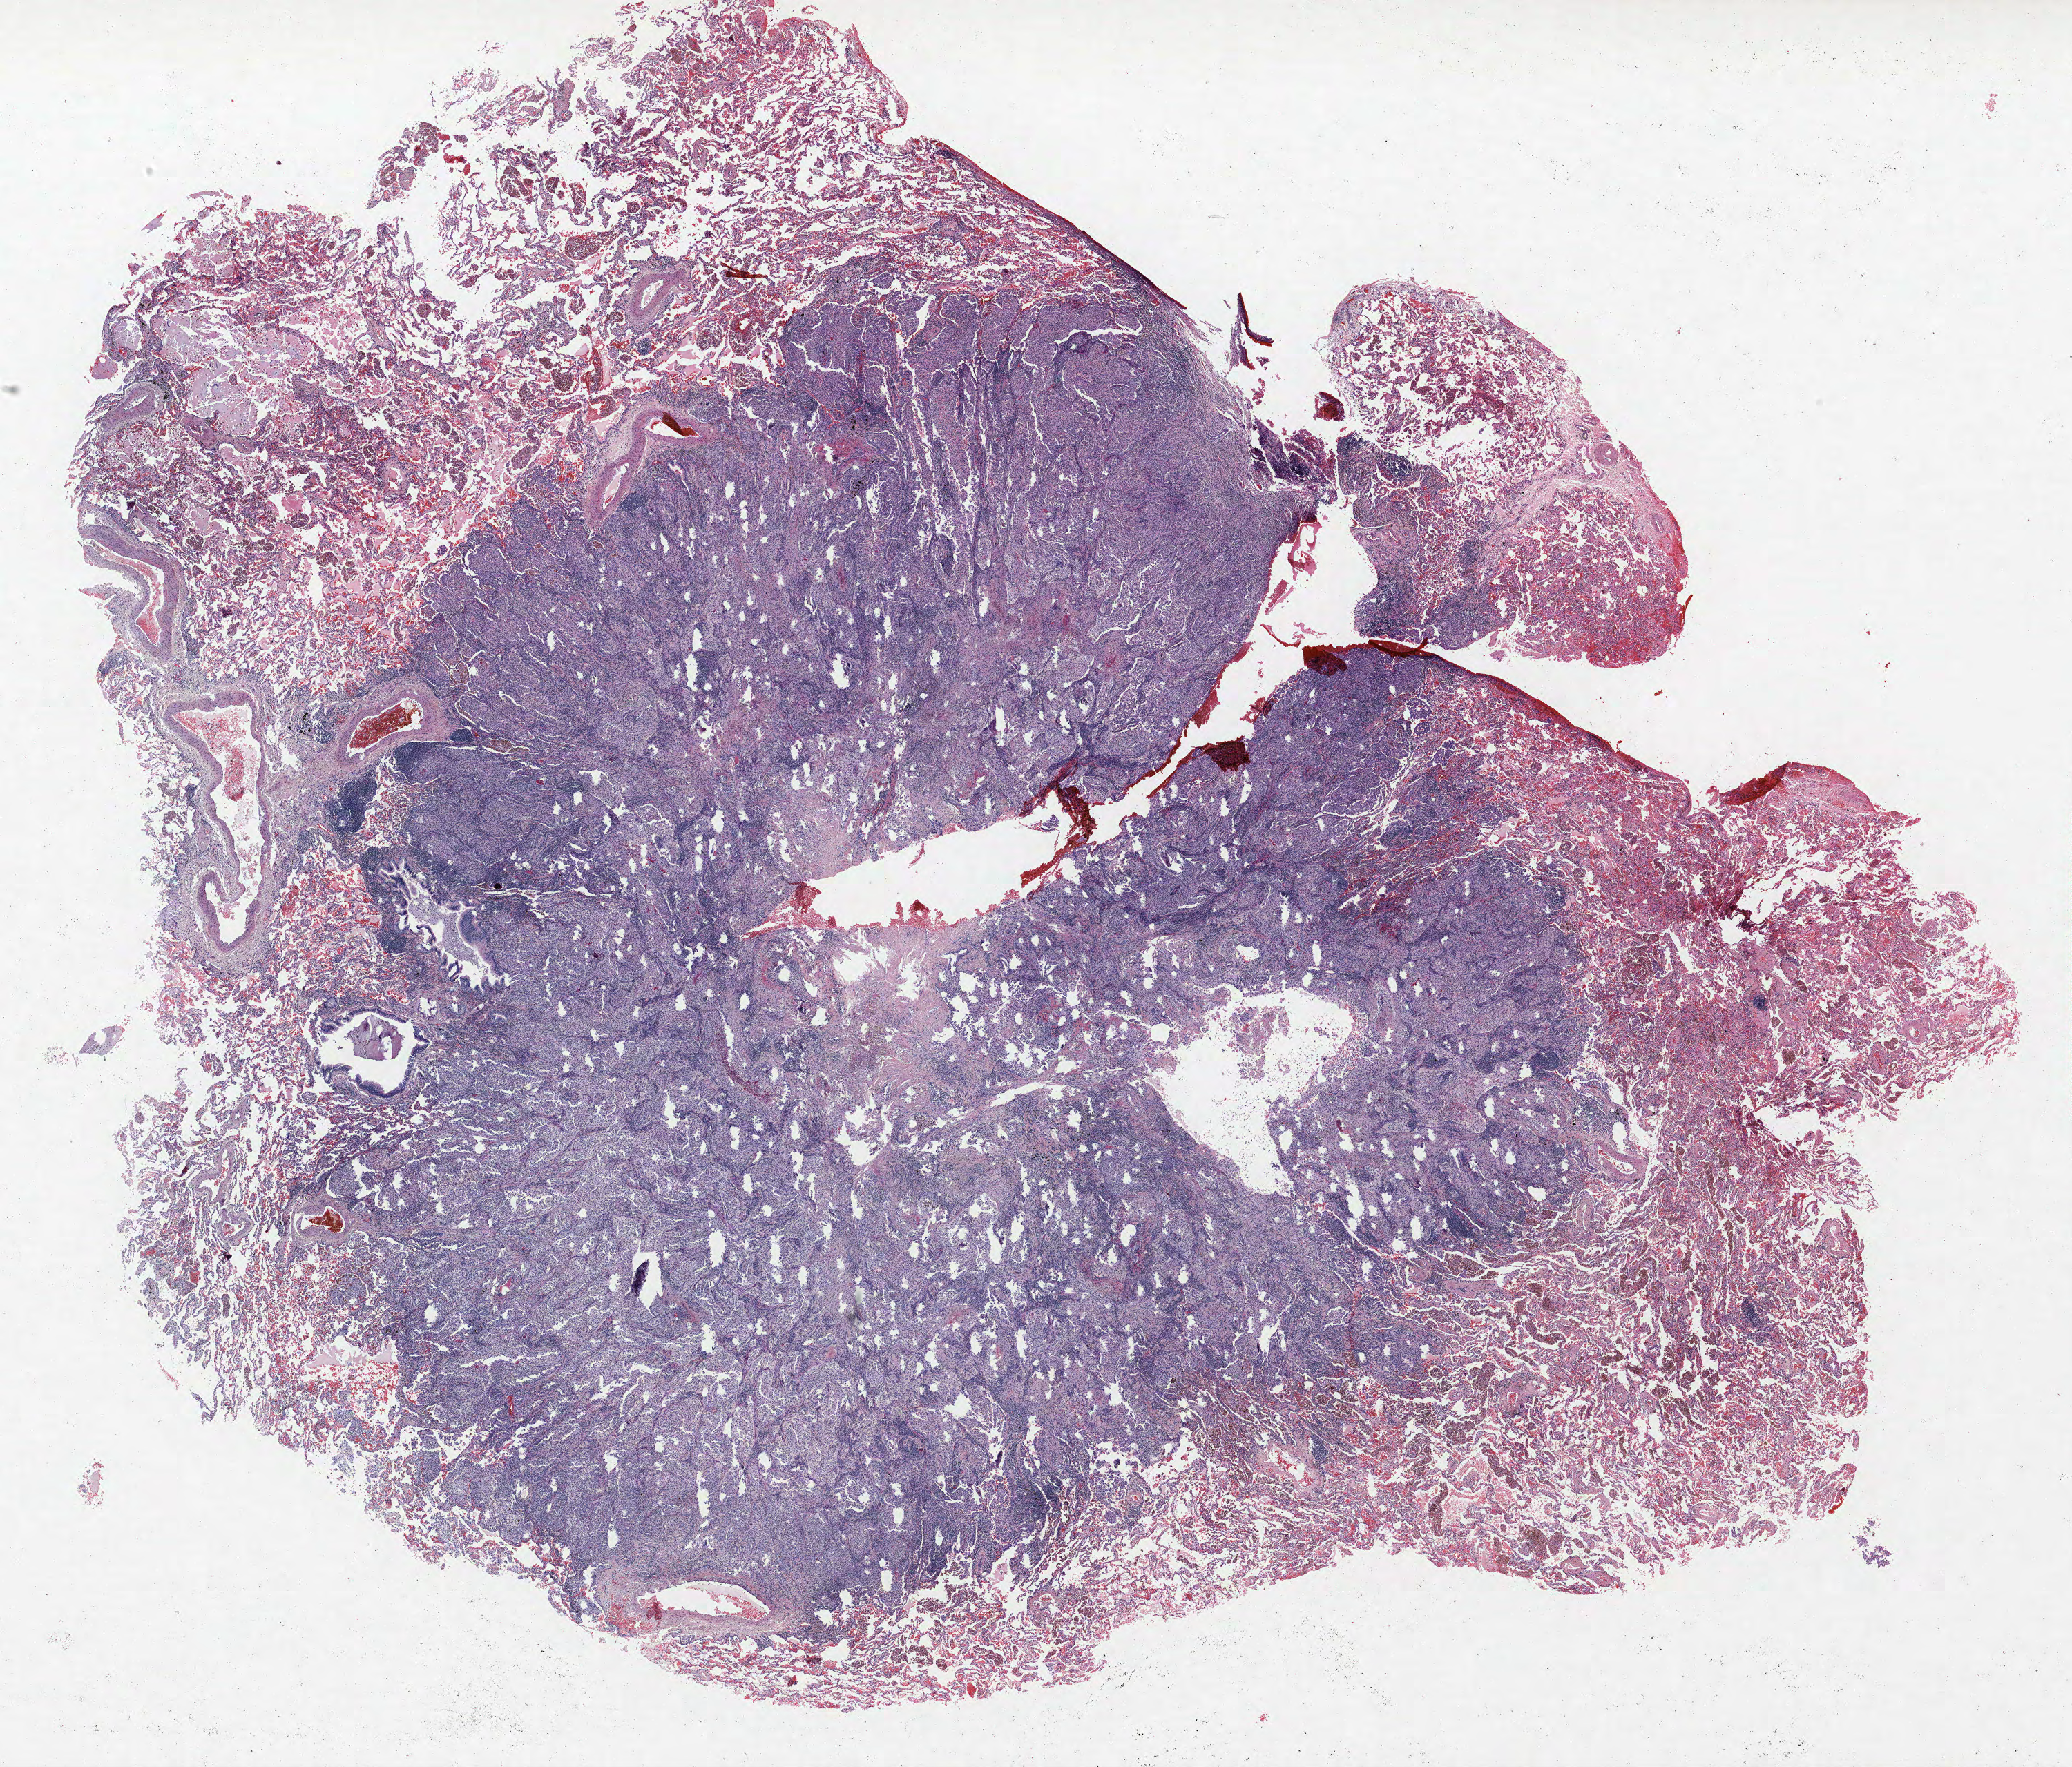
Hematoxylin and eosin (H&E) stained whole-slide image — a low-resolution overview of the entire scanned area, about 24.0 x 20.5 mm (acquisition: 40x scan). FFPE section. Lung tissue. Male patient, aged 63 at enrolment. Current smoker at enrolment. Grade: poorly differentiated (G3).
Stage (AJCC 6th edition): IA. Participant's lung-cancer diagnosis: Adenocarcinoma, NOS. Tumour size (pathology): 19 mm. Primary tumour location (clinical record): right lower lobe.